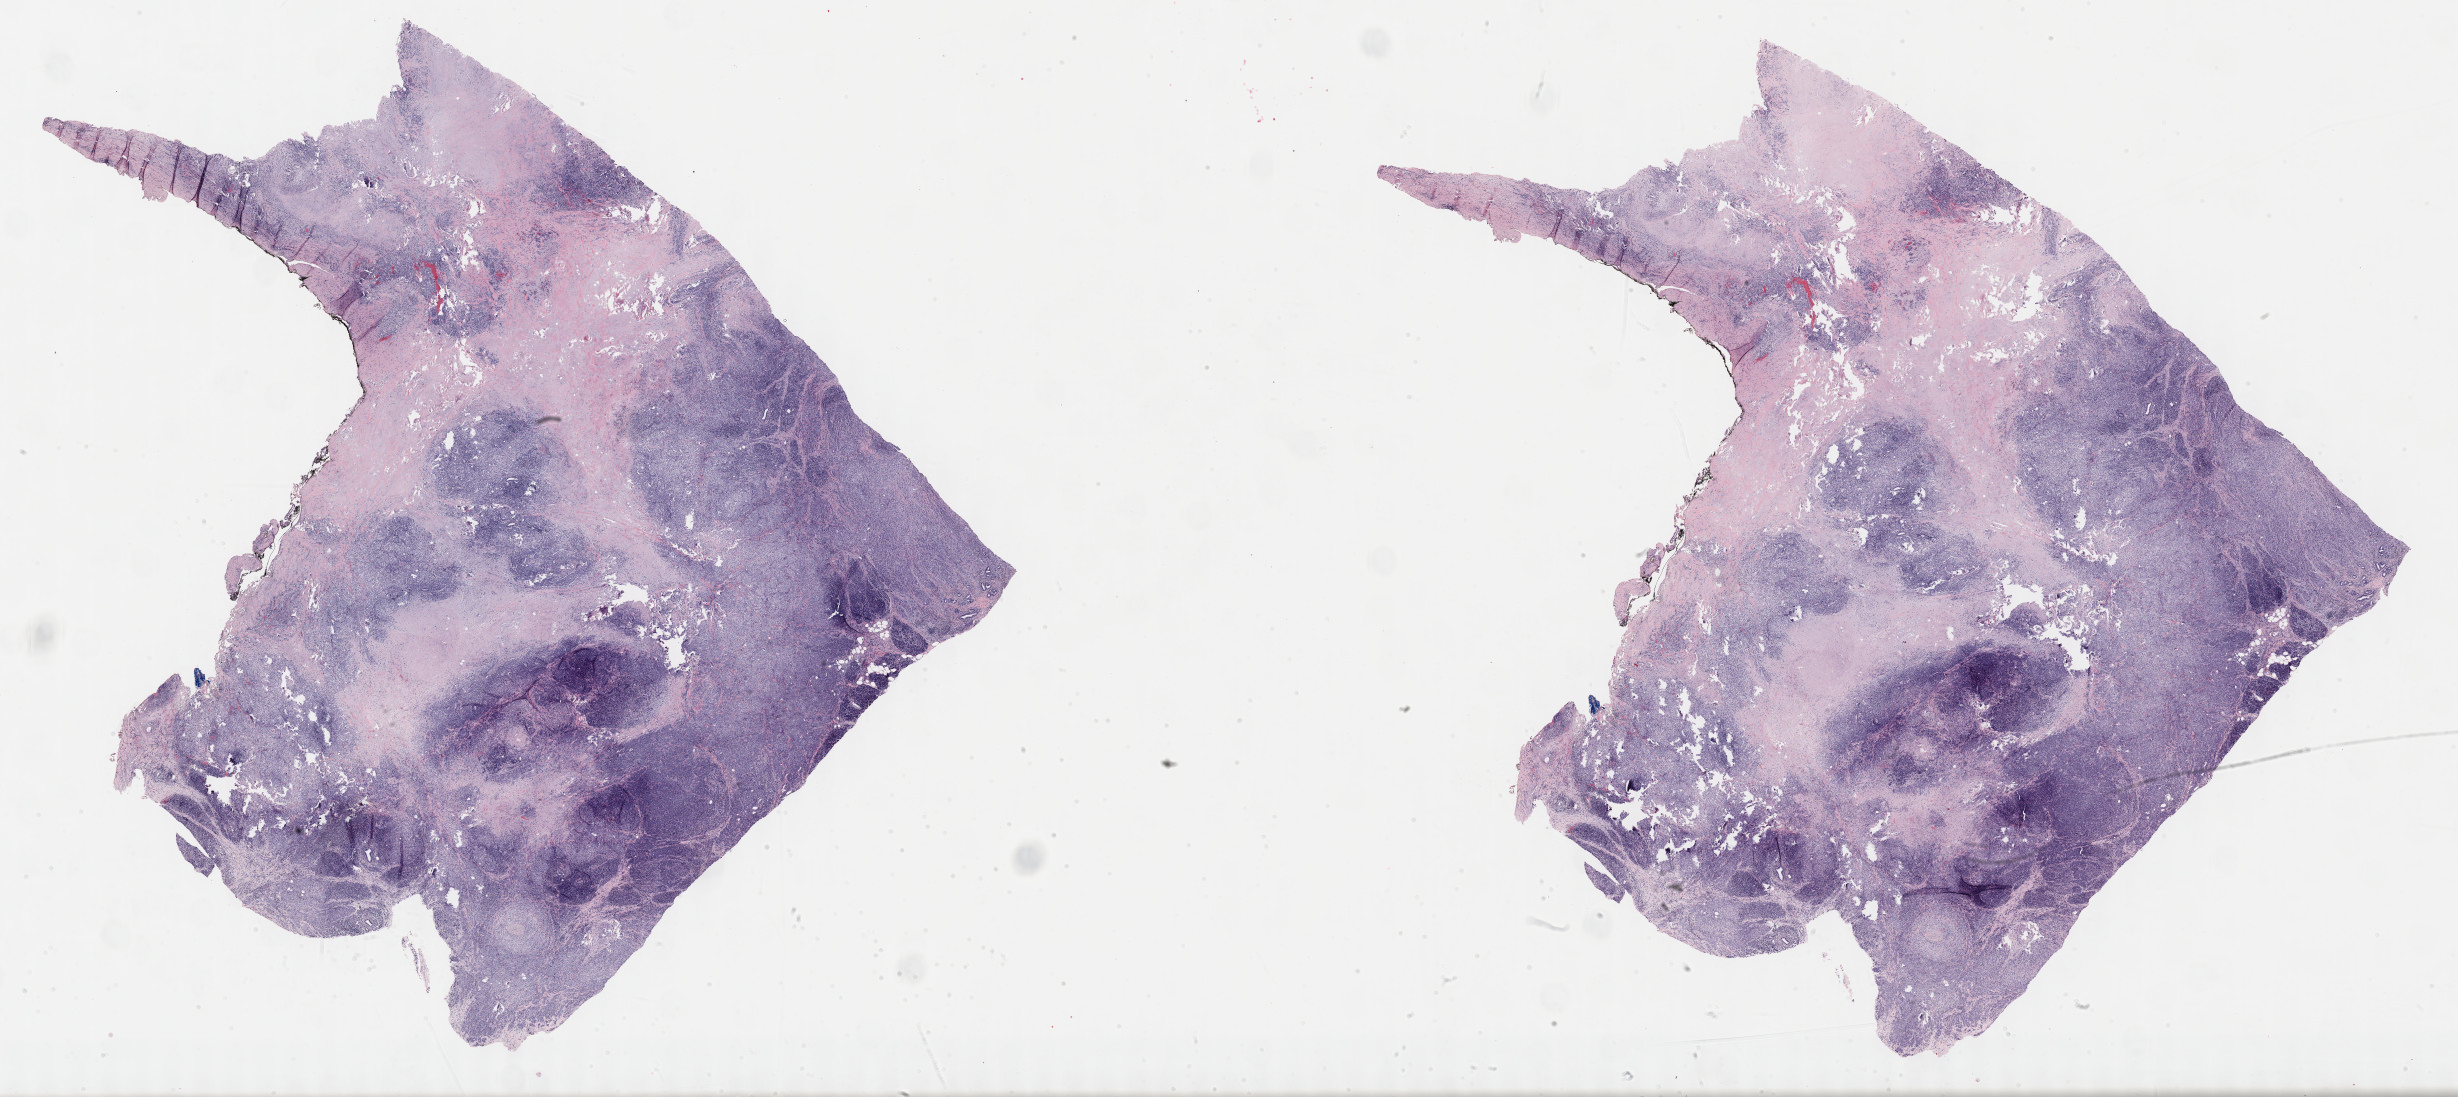
Whole-slide histology image, H&E, low-resolution overview of the scanned area, about 39.8 x 17.7 mm, formalin-fixed paraffin-embedded (FFPE) diagnostic section, pancreas, primary tumour sample. Female patient; age at initial diagnosis 48 years. Histologic grade: G3 (poorly differentiated).
Histologic diagnosis: Infiltrating duct carcinoma, NOS (head of pancreas). AJCC pathologic stage: IIB (7th edition).